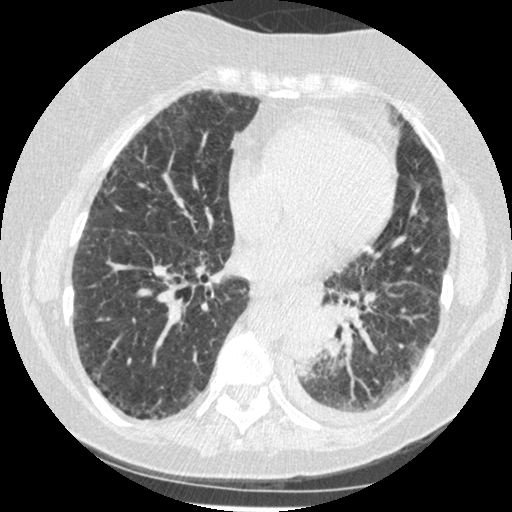
Low-dose screening chest CT, one axial slice. Slice 89 of 341 in the series (ordered by position). Reconstruction kernel STANDARD. Lung window (W 1500 / L -600 HU). 512 × 512 image matrix.
Annotated regions visible in this slice (manually delineated by an expert):
- lesion 1 (tumor, lower lobe of left lung): bounding box (x1, y1, x2, y2) in pixels: (290, 315, 326, 372)